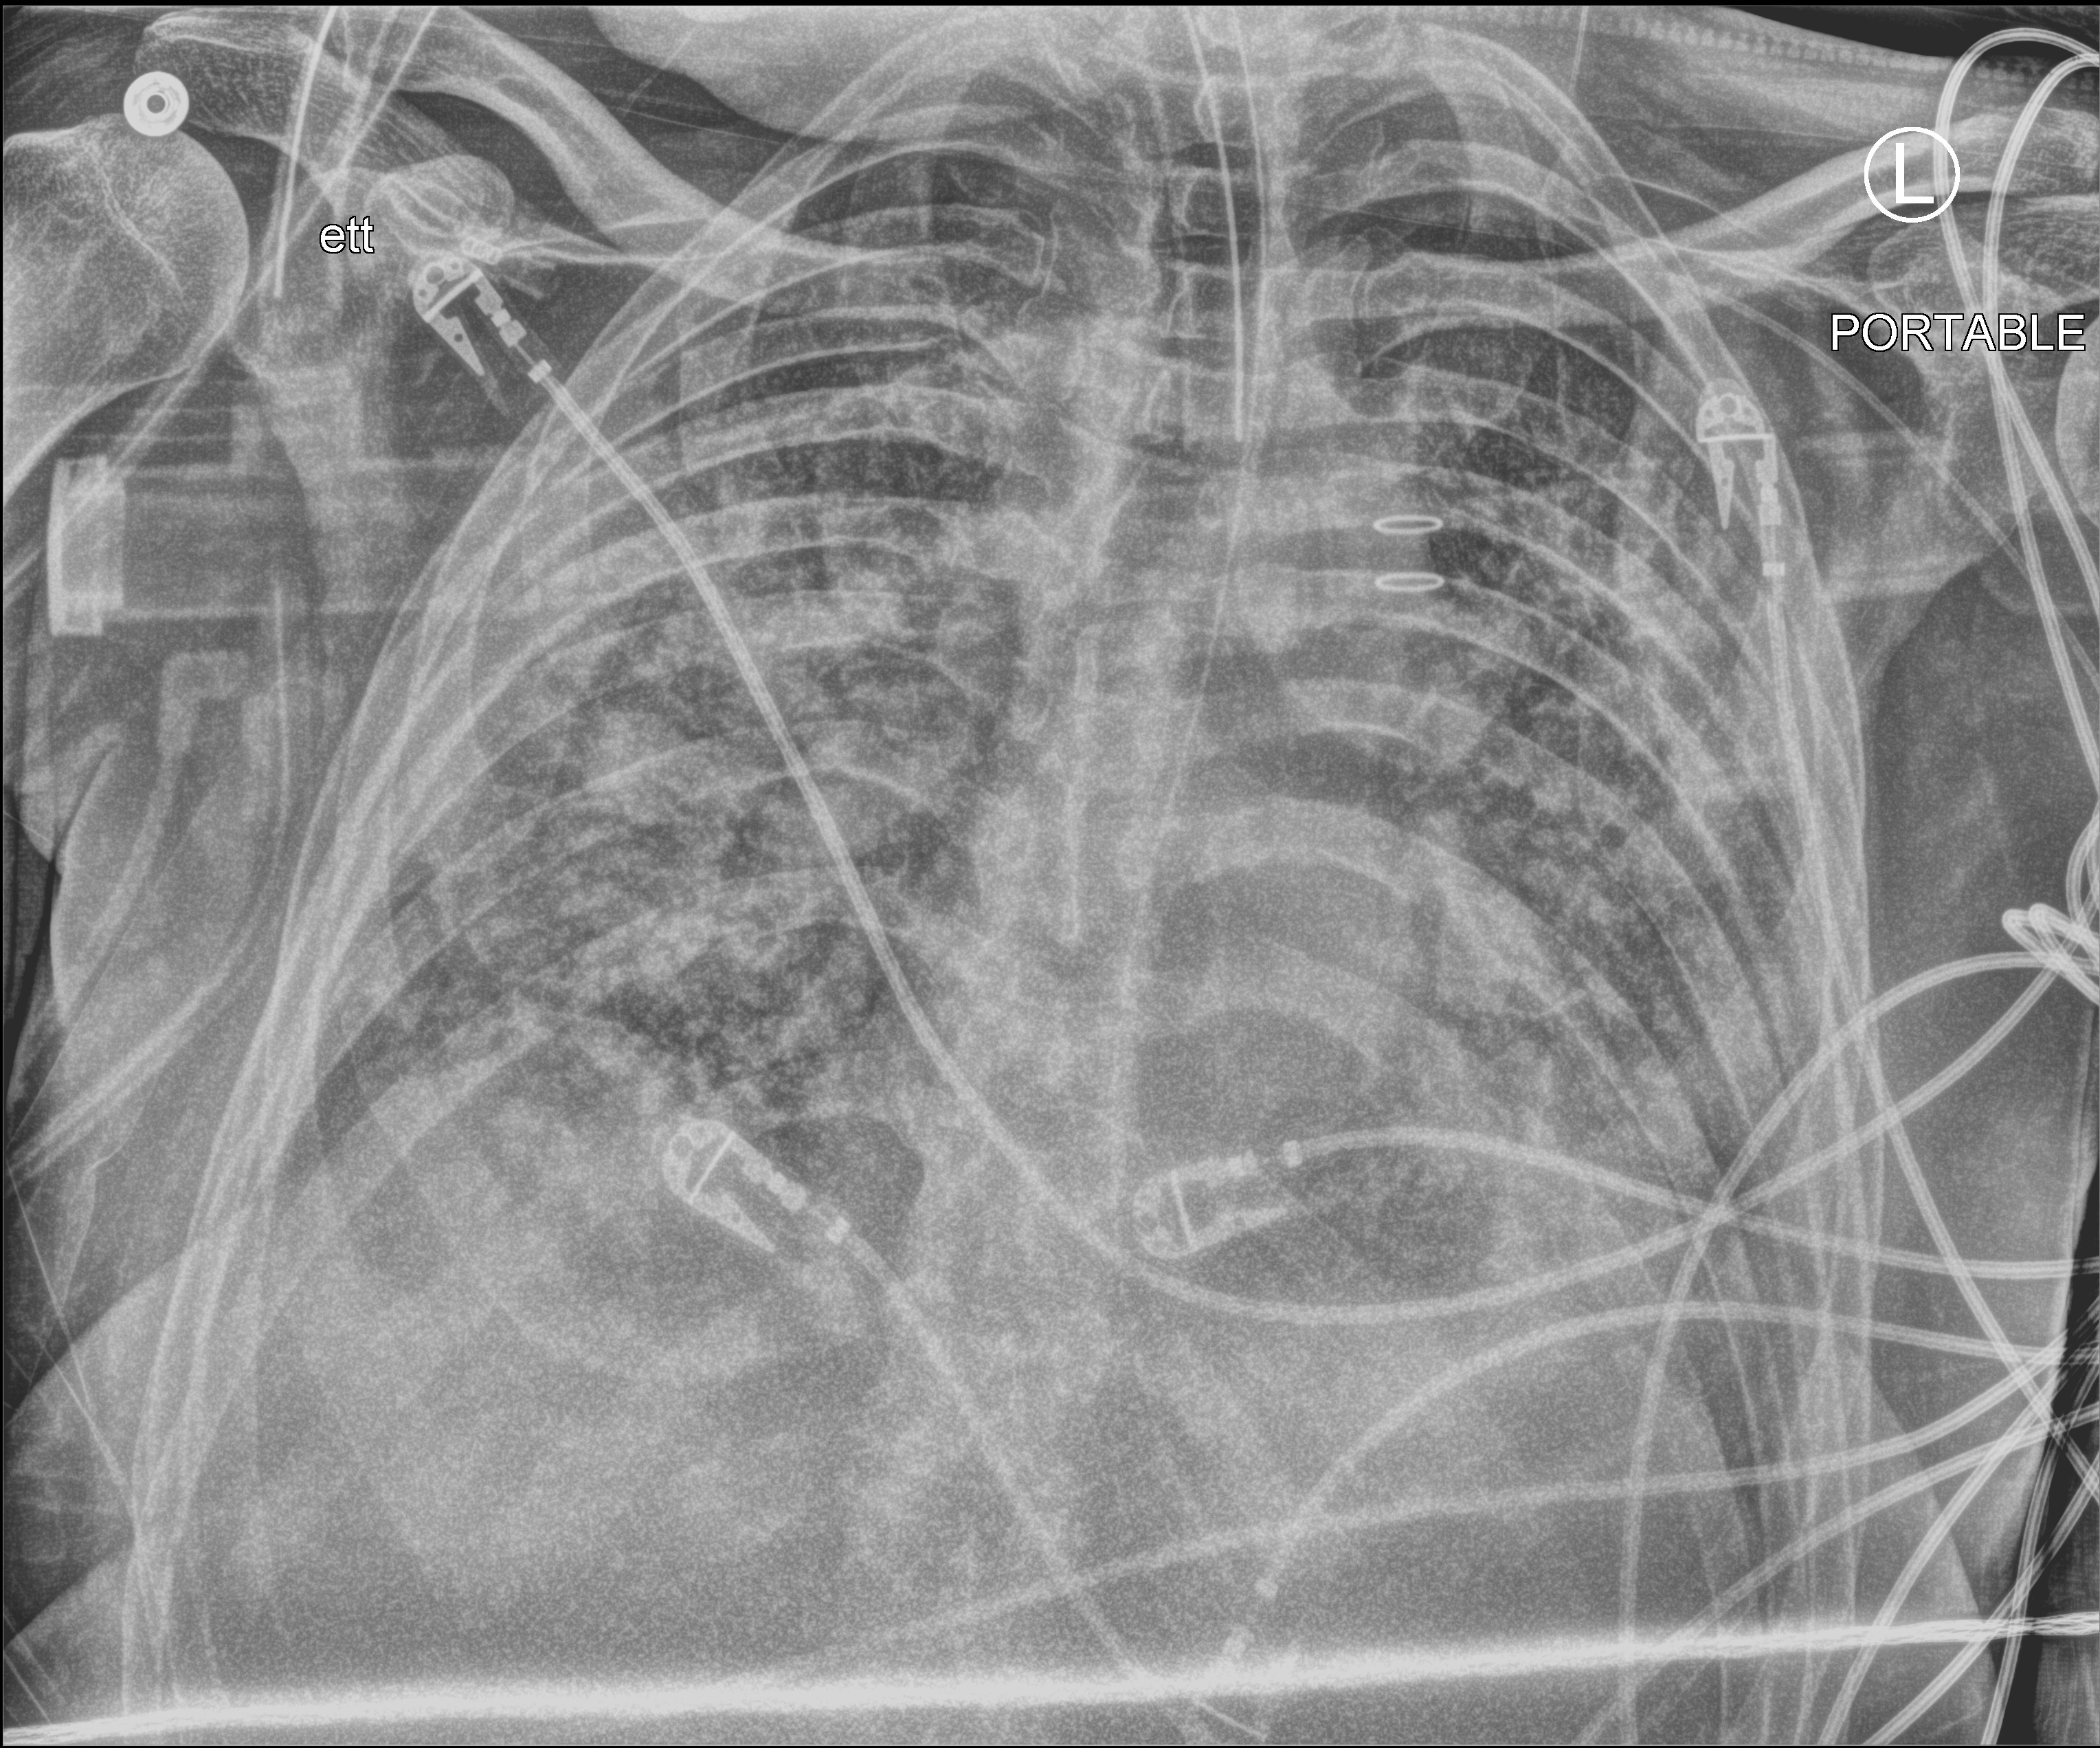
Chest X-ray (portable); anteroposterior (AP) projection. Male patient hospitalised with COVID-19, age 18–59 years.
Admission-level facts for this patient (not findings on this image; timing relative to this image not recorded): COPD (admission record): no; smoking status (admission record): never; admitted to intensive care during this hospital stay: yes.